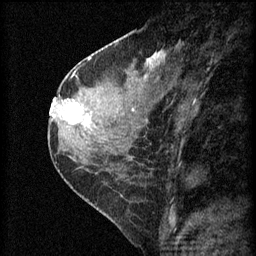
Breast MRI (dynamic contrast-enhanced), one sagittal slice; position 27 of 60 along the scan axis; 3 images stored at this slice position (order not interpretable as contrast timing); 1.5 T; TE 4.2 ms, TR 8.2 ms; 2 mm slice thickness; 256 × 256 image matrix. Patient: female, 45 years.
Outlined on this slice (semi-automatically segmented with operator editing):
- analysis volume of interest (the breast-tissue region the enhancement analysis was run in; not a lesion): bounding box (x1, y1, x2, y2) in pixels: (62, 98, 104, 139)
- tumour enhancement mask (voxels above the 70 % enhancement threshold inside the analysis volume of interest): (64, 100, 91, 125)